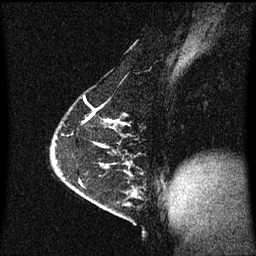
Breast MRI (dynamic contrast-enhanced), one sagittal slice. Position 37 of 60 along the scan axis. Dynamic contrast-enhanced series, image 2 of 3 at this slice position (ordered by acquisition). 1.5 T. TE 4.2 ms, TR 8.4 ms. 256 × 256 image matrix, field of view 200 × 200 mm. Patient: female, 63 years.
Outlined on this slice (semi-automatic segmentation, software-assisted and operator-edited):
- analysis volume of interest (the breast-tissue region the enhancement analysis was run in; not a lesion): box from (x=98, y=168) to (x=139, y=217) px
- tumour enhancement mask (voxels above the 70 % enhancement threshold inside the analysis volume of interest): (x=132, y=190)–(x=137, y=197)